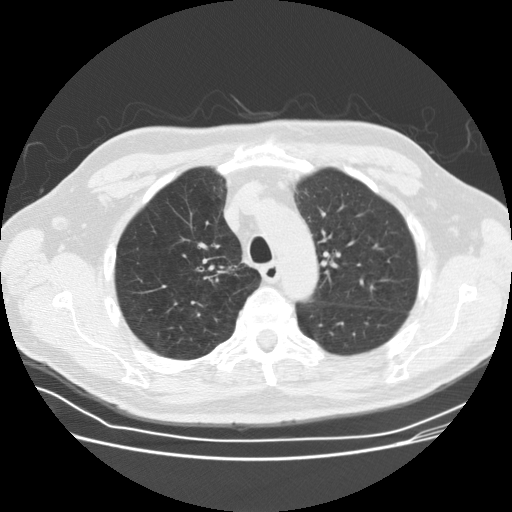
Axial slice from a low-dose chest CT screening exam; third screening round (two years after baseline); lung window (W 1500 / L -600 HU); 2.5 mm slice thickness; slice 120 of 164 in the series; 512 × 512 image matrix. Male, age 69 years at enrolment. Current smoker at enrolment.
Expert reader's lesion annotation, bounding box <221,255,261,288> (left, top, right, bottom; pixels). Reader record for this screening exam (exam-level; its link to the box is not recorded): non-calcified nodule or mass ≥4 mm, right upper lobe, 12 × 10 mm, spiculated (stellate) margins, soft tissue attenuation, pre-existing on the prior screen: yes; interval growth: yes. Lung cancer was diagnosed 36 days after this screen: squamous cell carcinoma, NOS, right upper lobe, moderately differentiated (G2), stage IA (AJCC 6th edition), 9 mm at pathology.